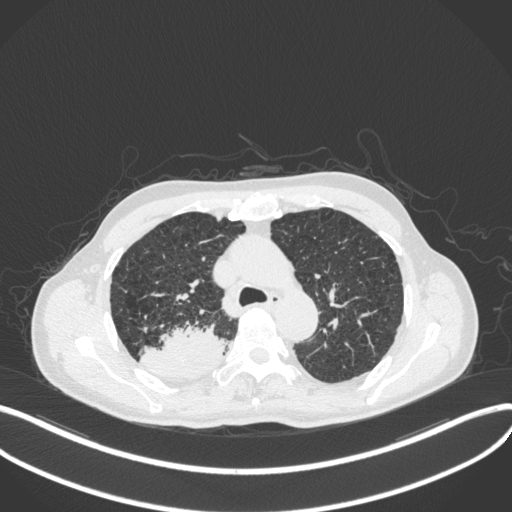
Chest CT, one axial slice. Position 320 of 423 along the scan axis. Reconstruction kernel B31f. 120 kVp. Lung window (W 1500 / L -600 HU). 1 mm slice thickness. 512 × 512 image matrix, field of view 400 × 400 mm. Male patient, age 79 years. From the clinical record (not read from this slice): clinical TNM (as recorded): T3 N0 M0.
Outlined on this slice (rectangle marked by the reading radiologist):
- lung tumour (recorded histology: adenocarcinoma): box from (x=137, y=322) to (x=228, y=378) px